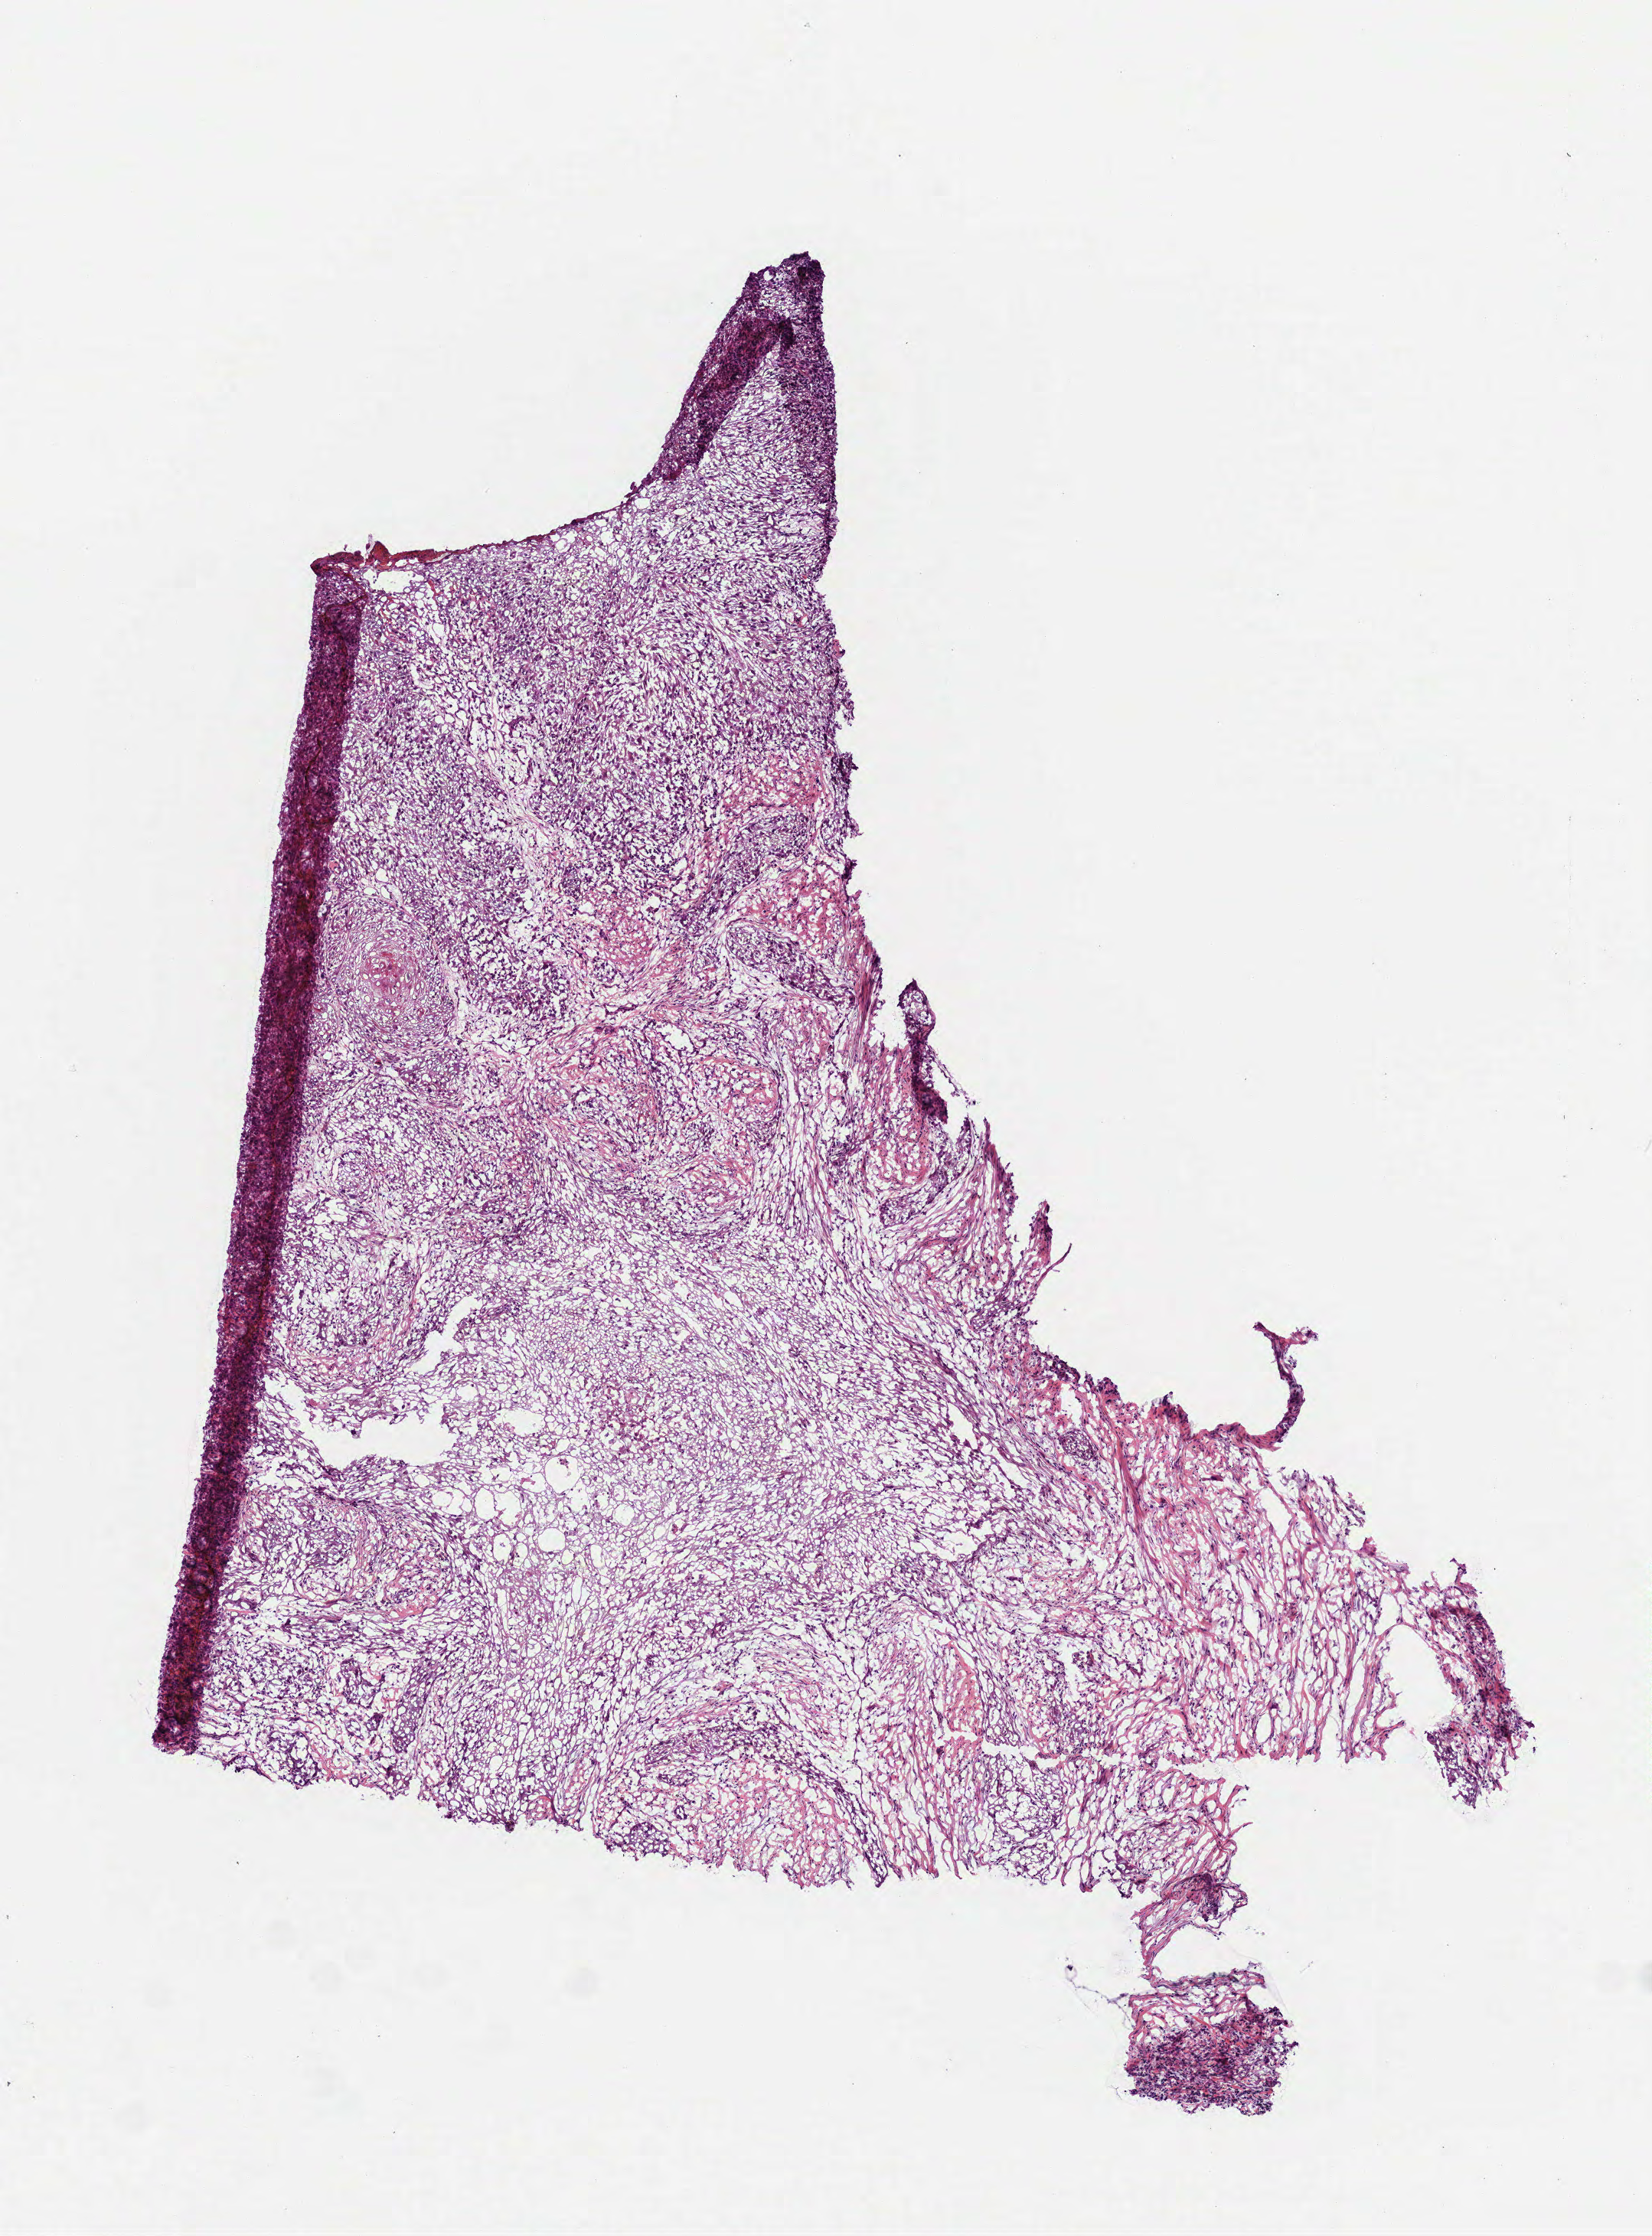
Whole-slide histology image, Hematoxylin and eosin (H&E) stained, low-resolution overview of the scanned area, about 4.4 x 5.9 mm. Frozen section from the top of the tissue portion. Primary tumour sample from the head and neck. Female, age 75 years at initial diagnosis. Histologic grade: G3 (poorly differentiated). Composition of this section per pathologist review: tumour cells 100%, tumour nuclei 85%, normal cells 0%, stromal cells 0%, necrosis 0%. Infiltration values recorded for this section: lymphocyte infiltration 7%, monocyte infiltration 0%, neutrophil infiltration 0%.
* TNM: T1 N0
* laterality: left
* lymph nodes positive (case pathology): 0 of 15 examined
* AJCC pathologic stage: I
* pathologic diagnosis: Squamous cell carcinoma, NOS (mouth, NOS)